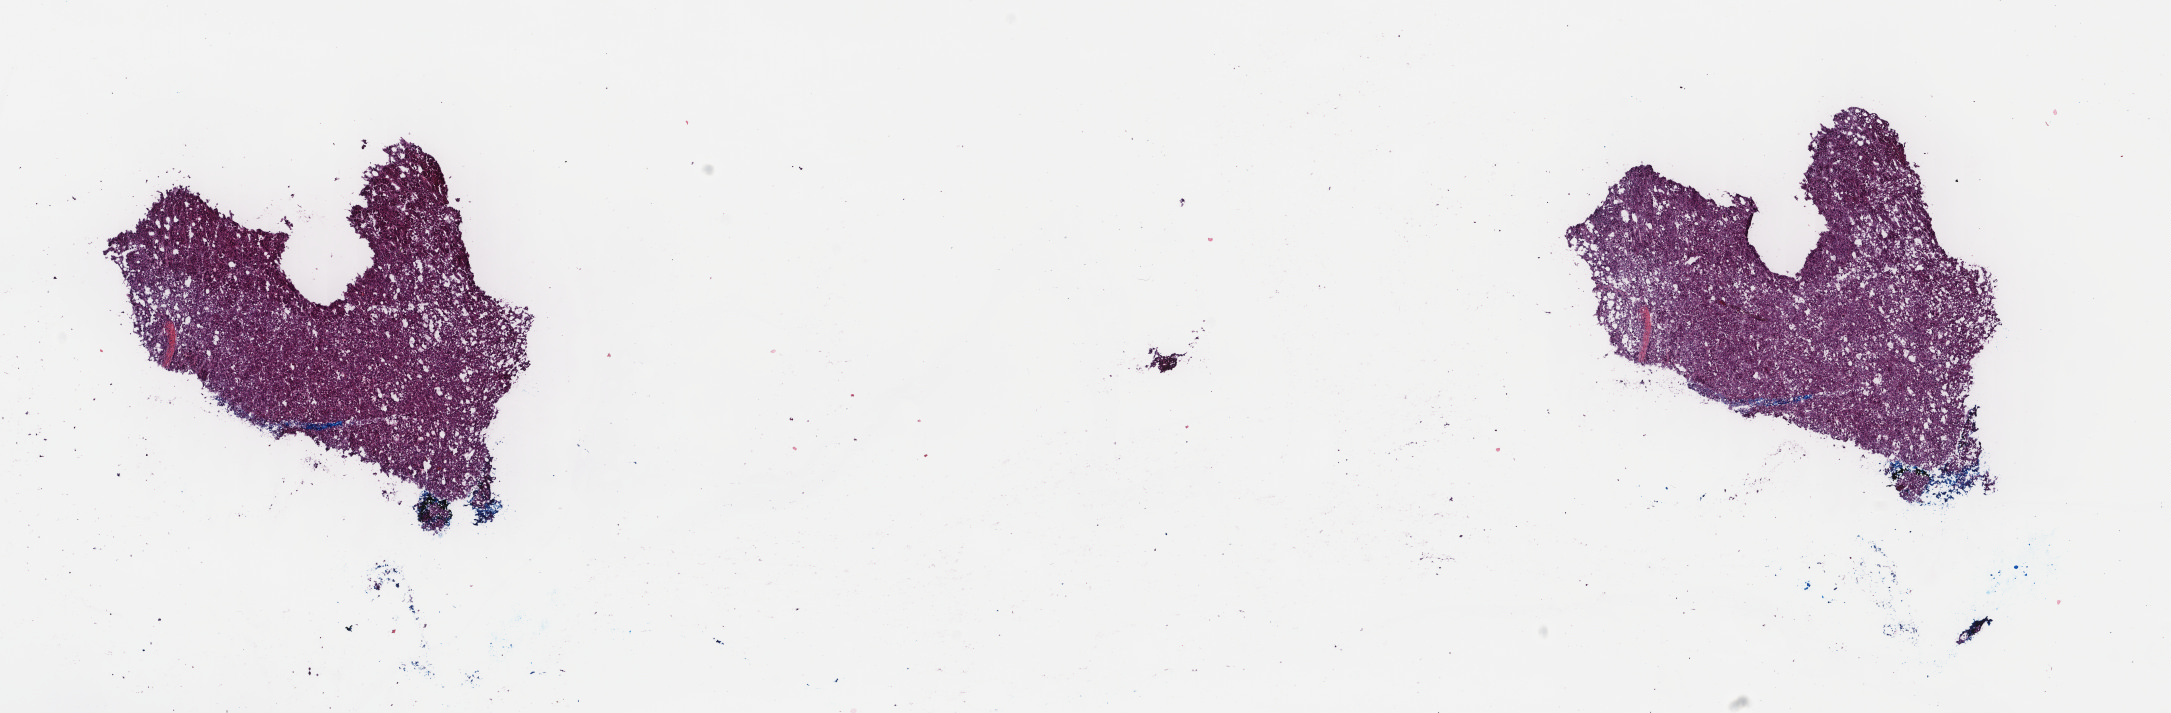
Whole-slide histology image, Hematoxylin and eosin (H&E) stained — whole scanned area (about 17.2 x 5.7 mm, from a 40x scan) shown as a low-resolution overview. Frozen section. Liver, primary tumour sample. Male, age 80 years at initial diagnosis. Histologic grade: G2 (moderately differentiated). Slide review estimates, as recorded: tumour cells 95%, tumour nuclei 97%, normal cells 0%, stromal cells 5%, necrosis 0%. Infiltration values recorded for this section: lymphocyte infiltration 1%, monocyte infiltration 0%, neutrophil infiltration 0%.
- TNM: T1 N0 MX
- histologic diagnosis: Hepatocellular carcinoma, NOS
- AJCC pathologic stage: I